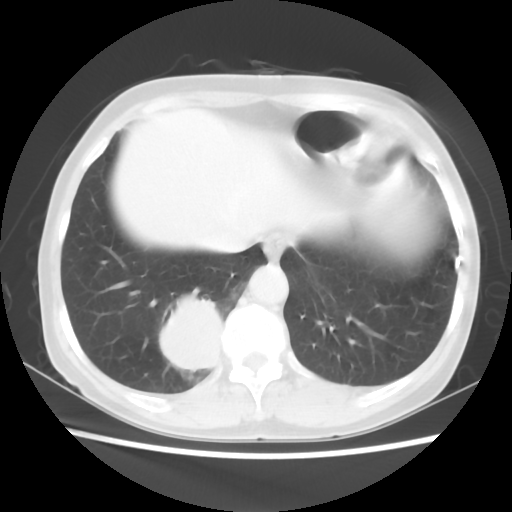
Chest CT, one axial slice; position 12 of 56 along the scan axis; lung window (W 1500 / L -600 HU); 5 mm slice thickness; 512 × 512 image matrix. Patient: female, 66 years. Case-level facts recorded for this patient, not image findings: clinical TNM (as recorded): T2 N3 M0.
Annotated regions visible in this slice (rectangle marked by the reading radiologist):
- lung tumour (recorded histology: small cell carcinoma): box from (x=153, y=288) to (x=231, y=385) px